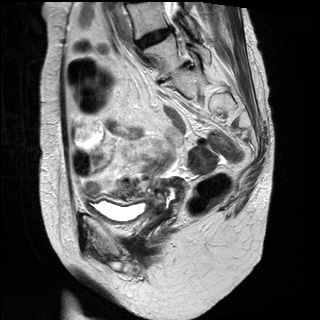
Pelvic MRI for cervical cancer, one sagittal slice. Position 12 of 31 along the scan axis. T2-weighted. 1.5 T. TE 89 ms, TR 3890 ms. 4 mm slice thickness. 320 × 320 image matrix, field of view 260 × 260 mm. Patient: female, 61 years.
Structures marked on this image (expert manual segmentation):
- uterus and cervix: box from (x=151, y=176) to (x=186, y=215) px